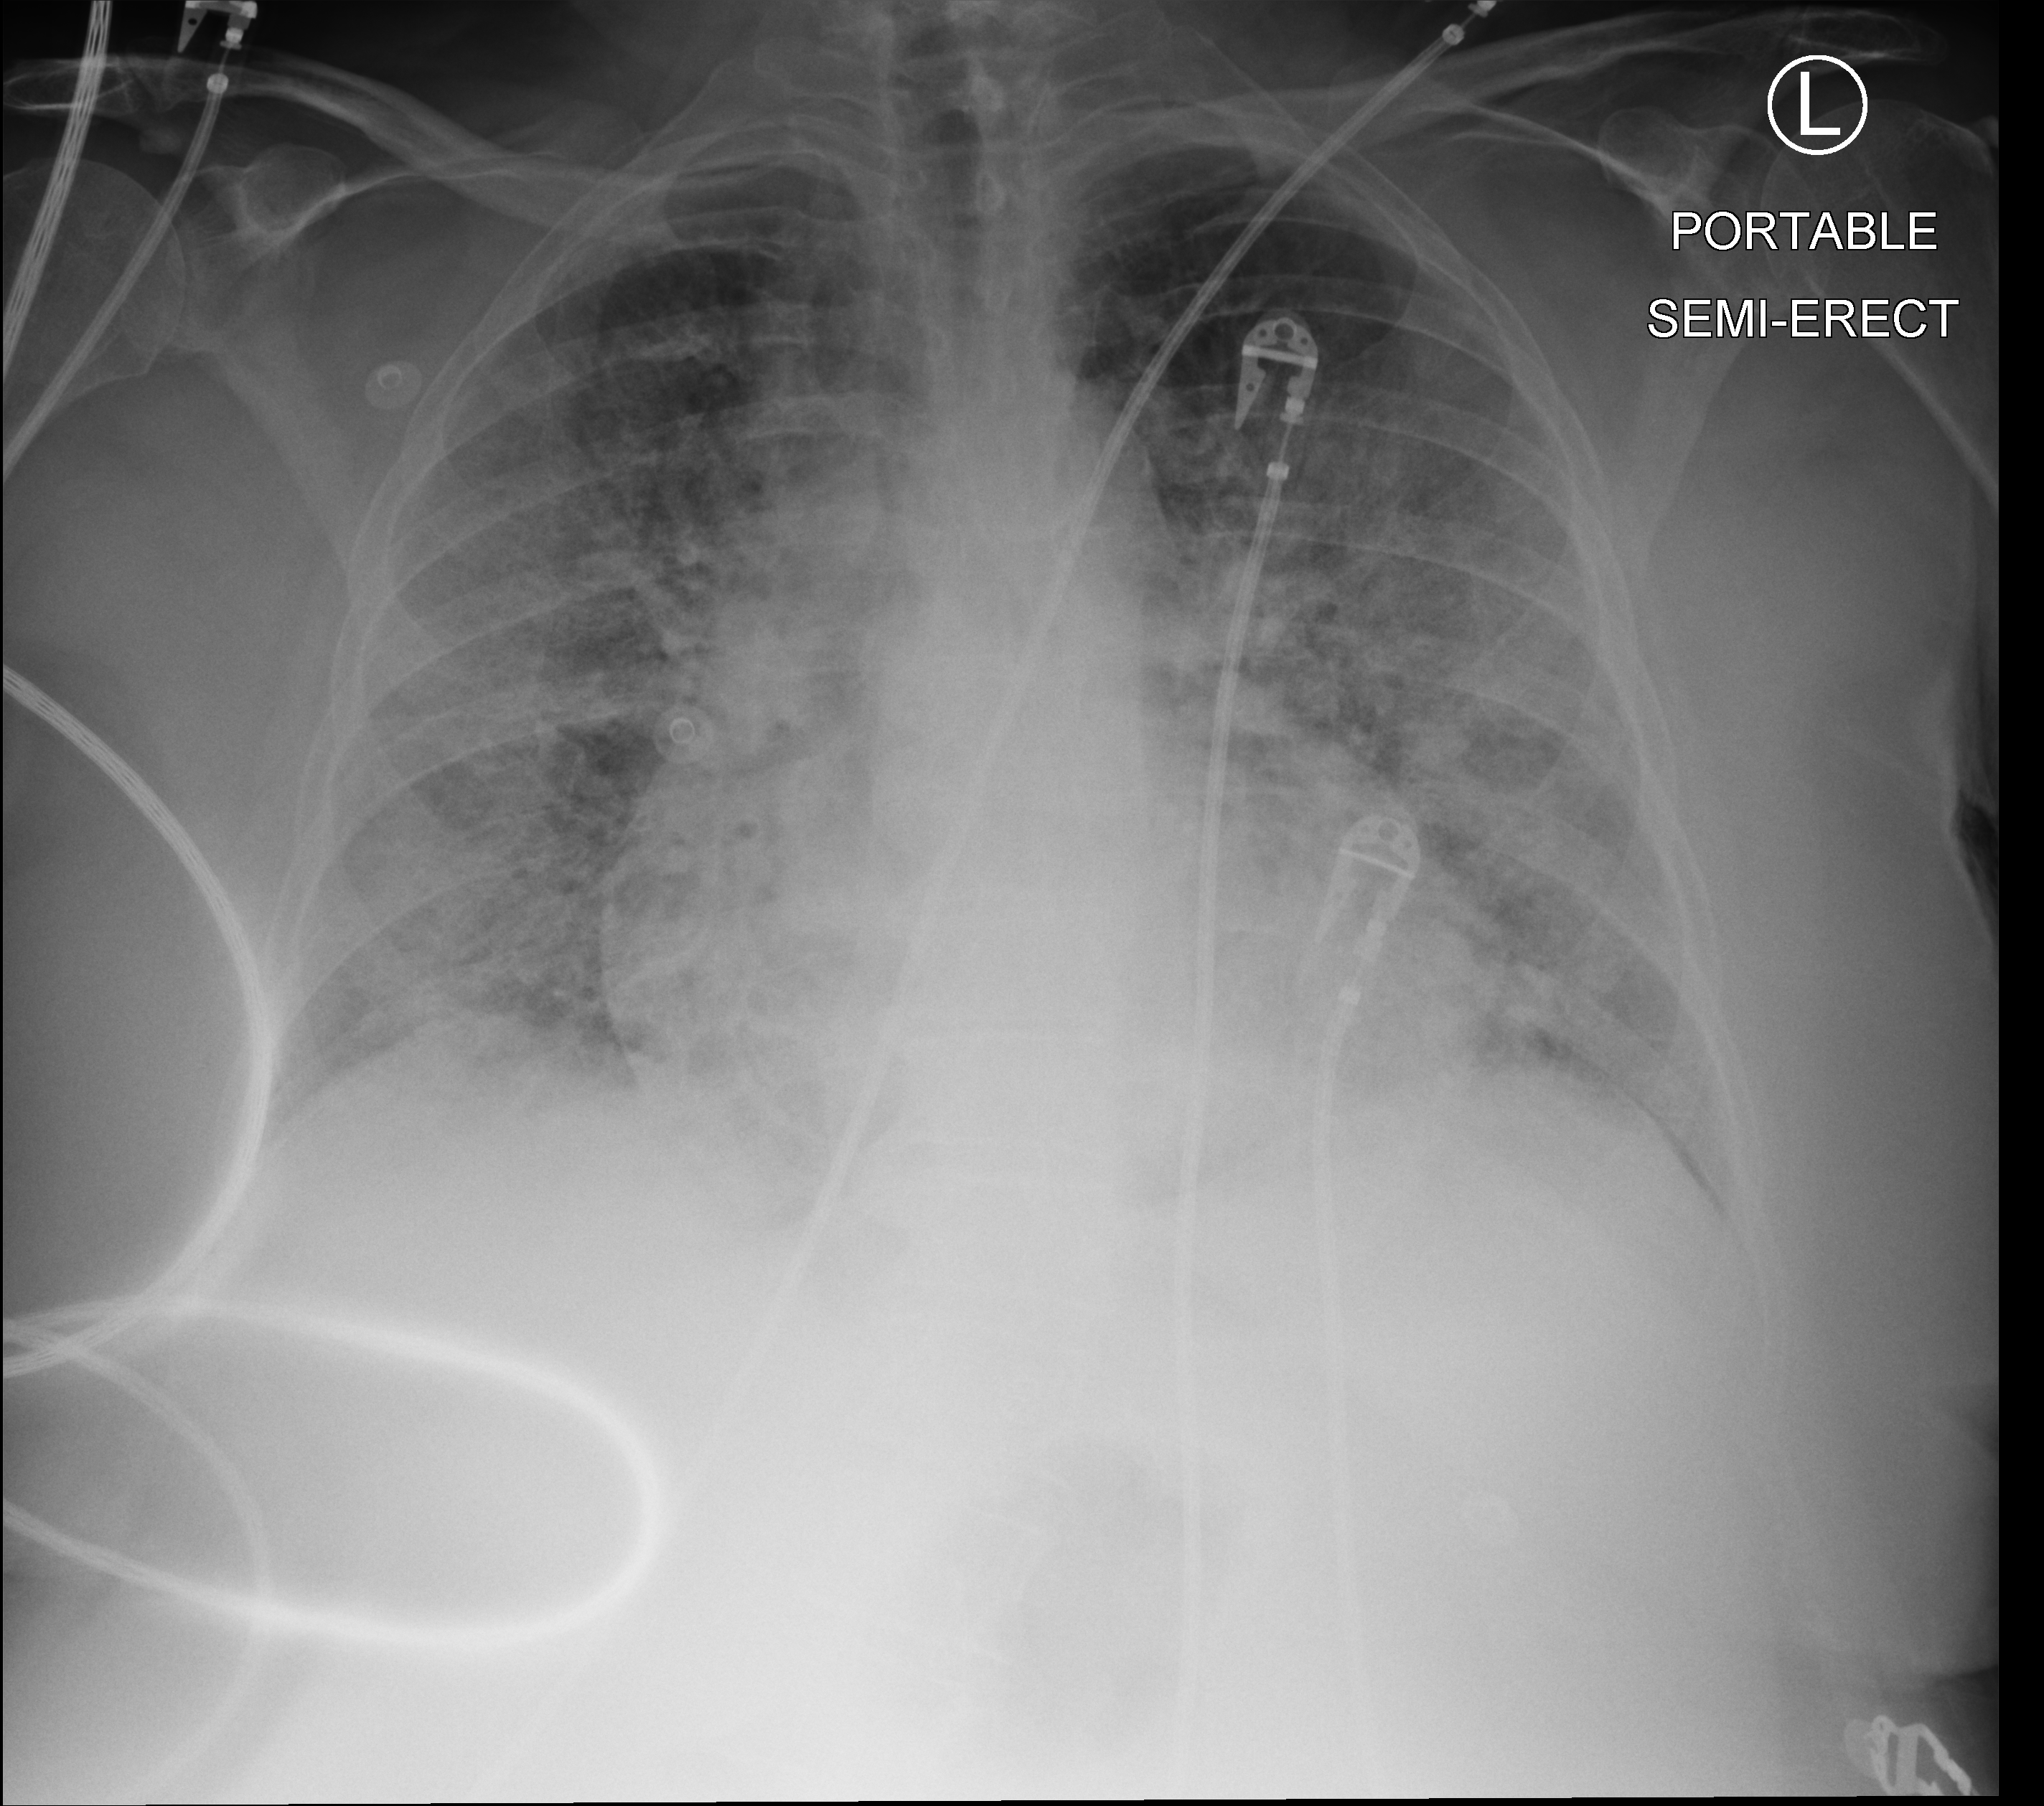
Portable chest radiograph, anteroposterior (AP) projection. Female patient hospitalised with COVID-19, age 75–90 years.
Admission-level facts for this patient (not findings on this image; timing relative to this image not recorded): mechanically ventilated during this hospital stay: yes.